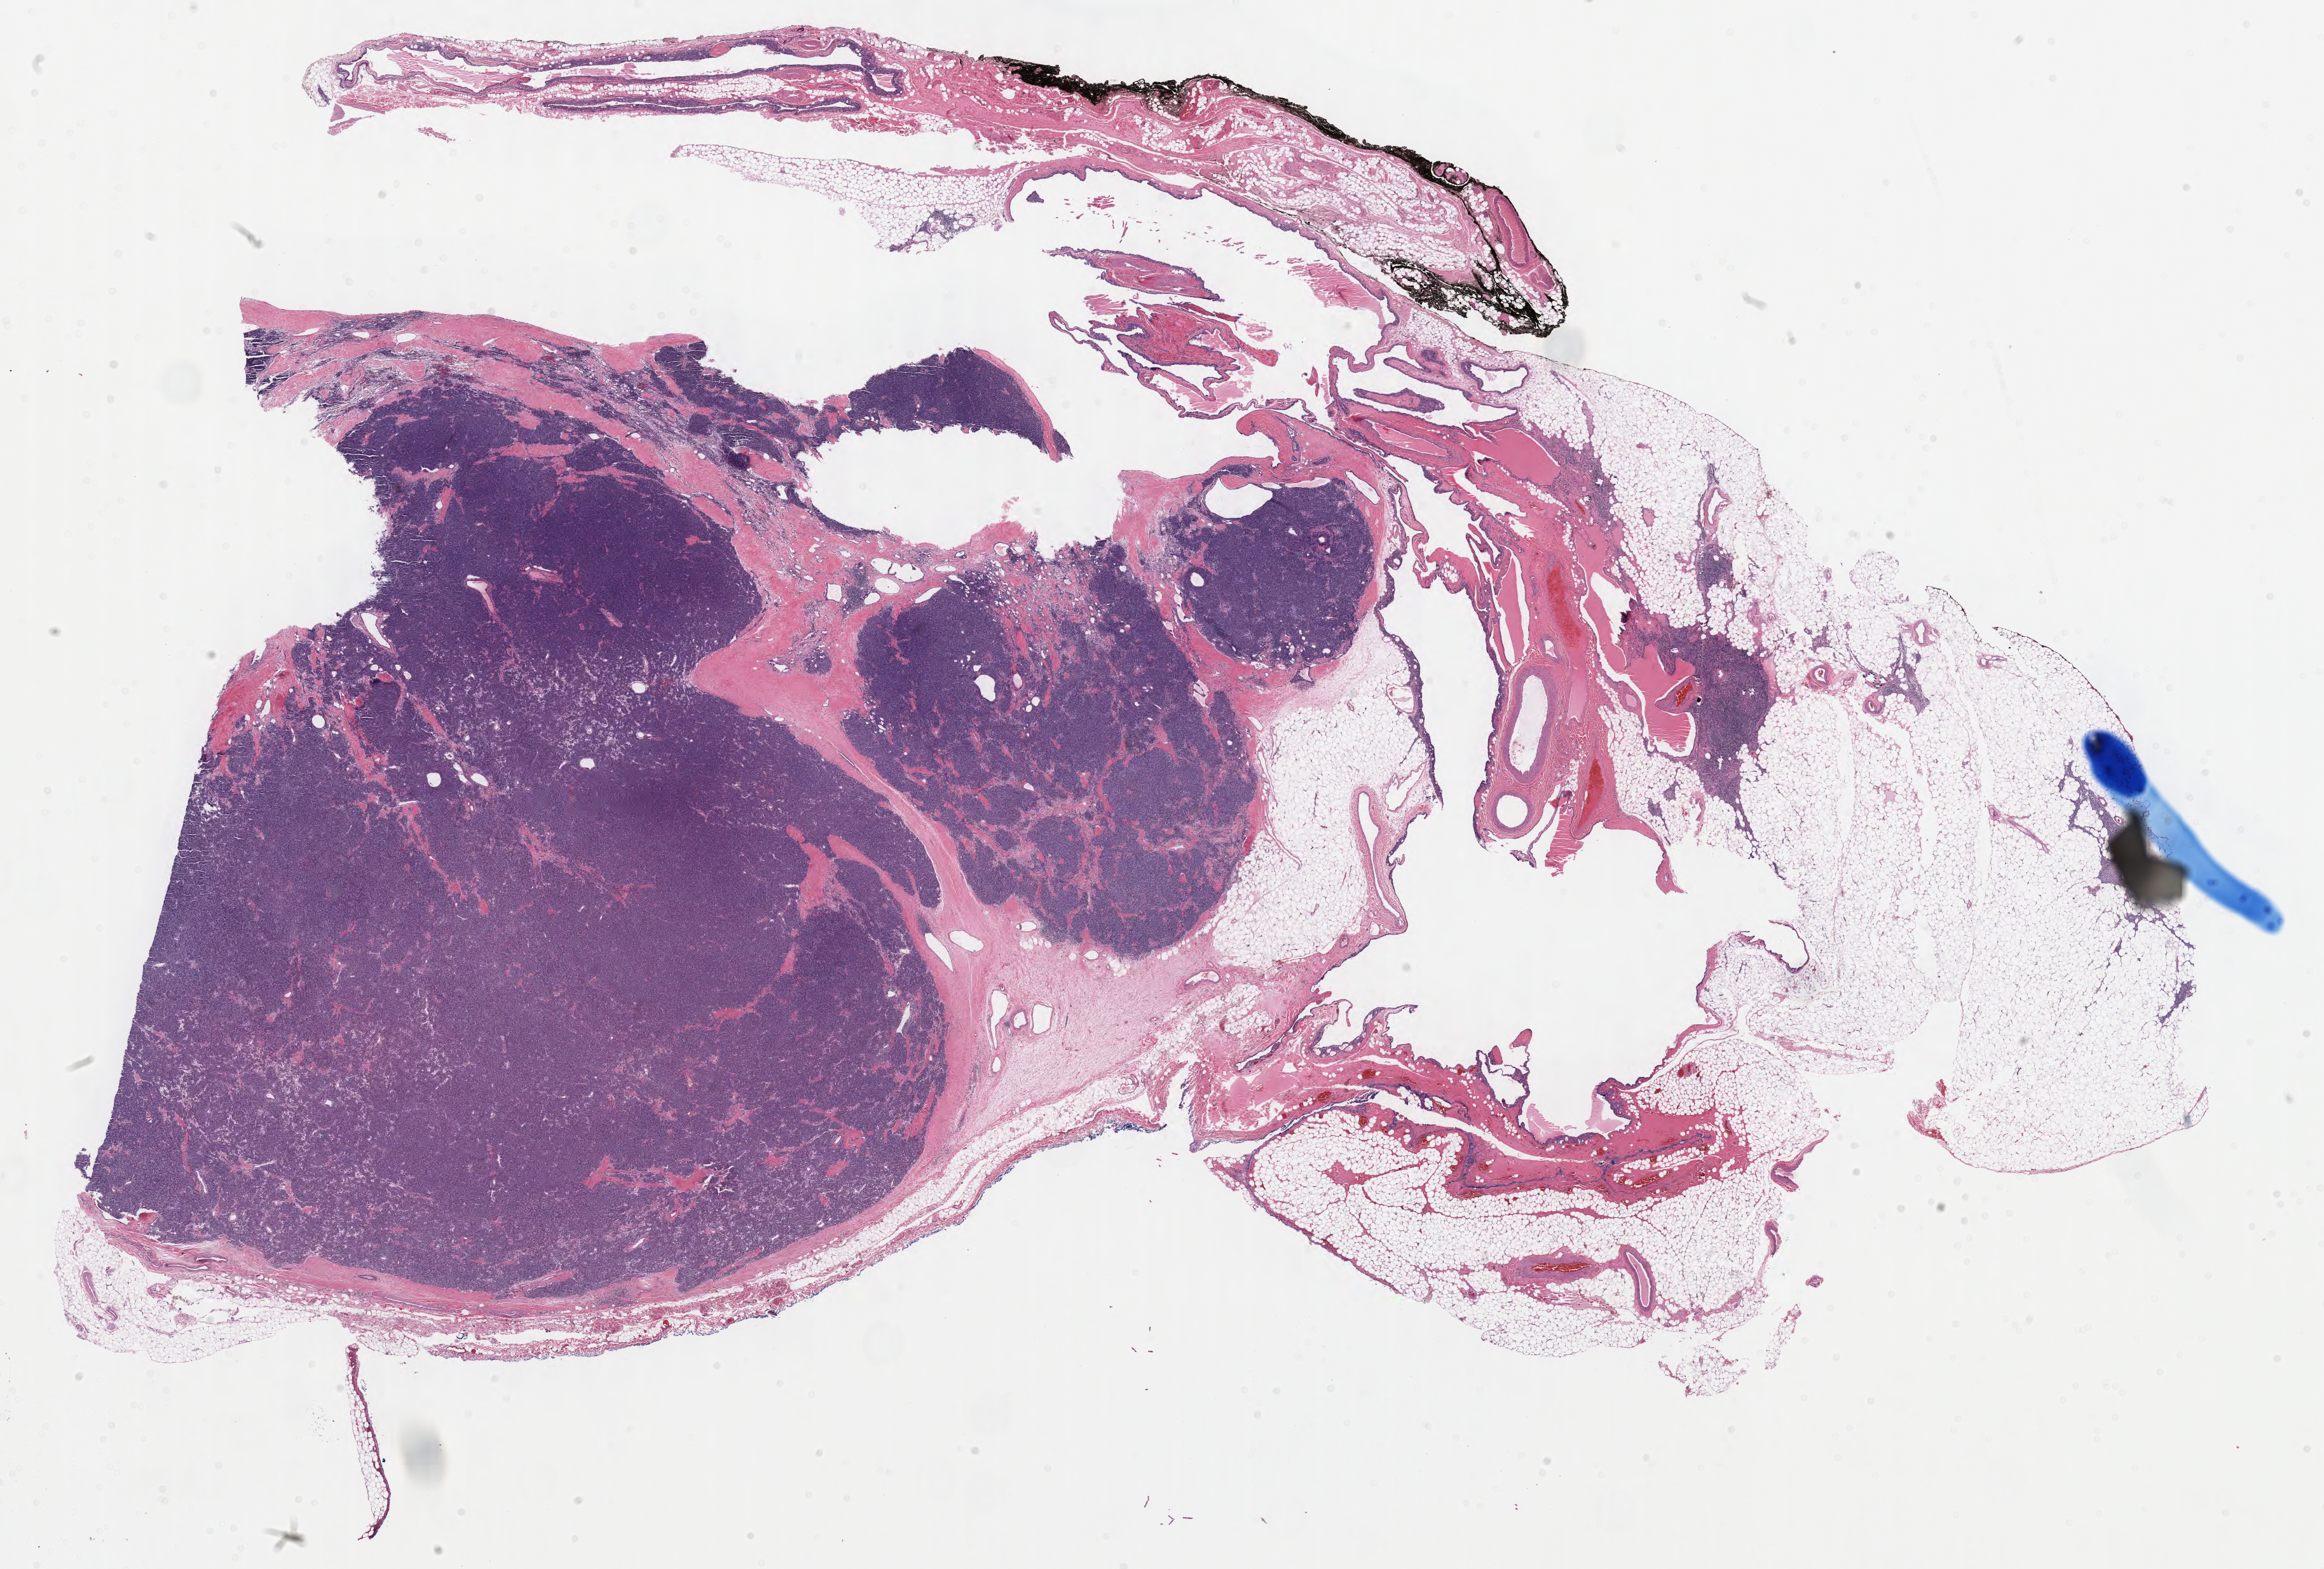
Whole-slide histology image, Hematoxylin and eosin (H&E) stained — a low-resolution overview of the entire scanned area, about 29.0 x 19.6 mm, formalin-fixed paraffin-embedded (FFPE) diagnostic section, thymus, primary tumour sample. Male, age 52 years at initial diagnosis.
Diagnosis: Thymoma, type A, malignant.